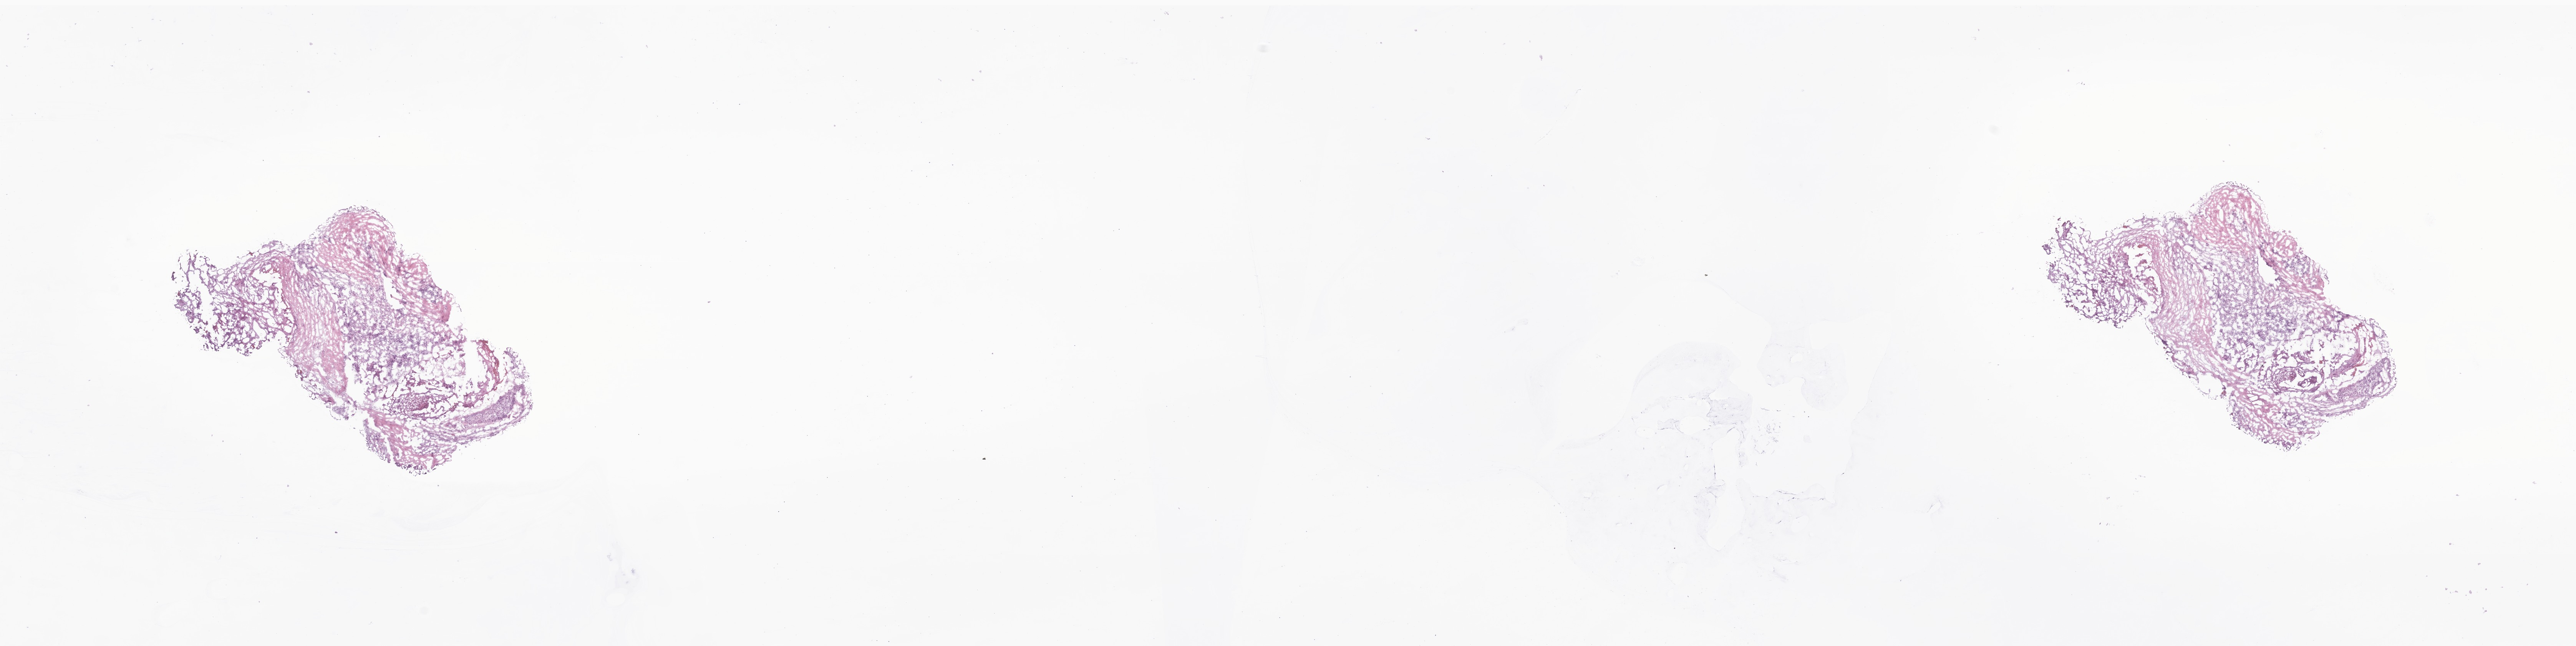
Whole-slide image, H&E stain of tumor tissue from the short bone of lower limb, whole scanned area (about 28.3 x 7.1 mm) shown as a low-resolution overview, frozen section (OCT-embedded). Male patient, age 184 months (15 years 4 months).
- recorded diagnosis: Sarcoma, NOS